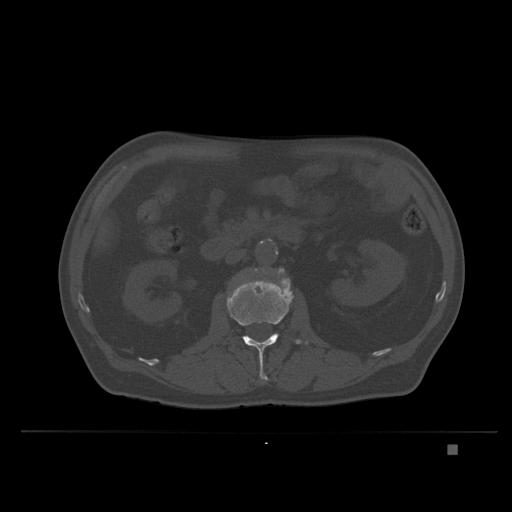
CT including the spine, one axial slice. Position 115 of 435 along the scan axis. Bone window (W 1800 / L 400 HU). 1.5 mm slice thickness. 512 × 512 image matrix, field of view 434 × 434 mm. Patient: male, 73 years. Case-level facts recorded for this patient, not image findings: primary cancer: skin.
Structures marked on this image (semi-automatic segmentation, software-assisted and operator-edited):
- L2 vertebra: bounding box [x1, y1, x2, y2] px = [226, 273, 308, 384]
- L3 vertebra: [279, 268, 284, 272]